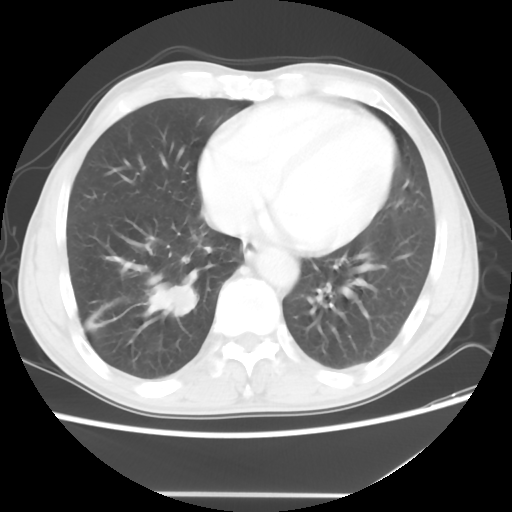
Chest CT, one axial slice. Slice 18 of 56 in the series (ordered by position). 120 kVp. Lung window (W 1500 / L -600 HU). 5 mm slice thickness. 512 × 512 image matrix, field of view 344 × 344 mm. Patient: male, 65 years. From the clinical record (not read from this slice): clinical TNM (as recorded): T1c N3 M0; histopathological grade: G3.
Structures marked on this image (bounding box drawn by a radiologist):
- lung tumour (recorded histology: small cell carcinoma): bounding box [x1, y1, x2, y2] px = [148, 277, 200, 314]